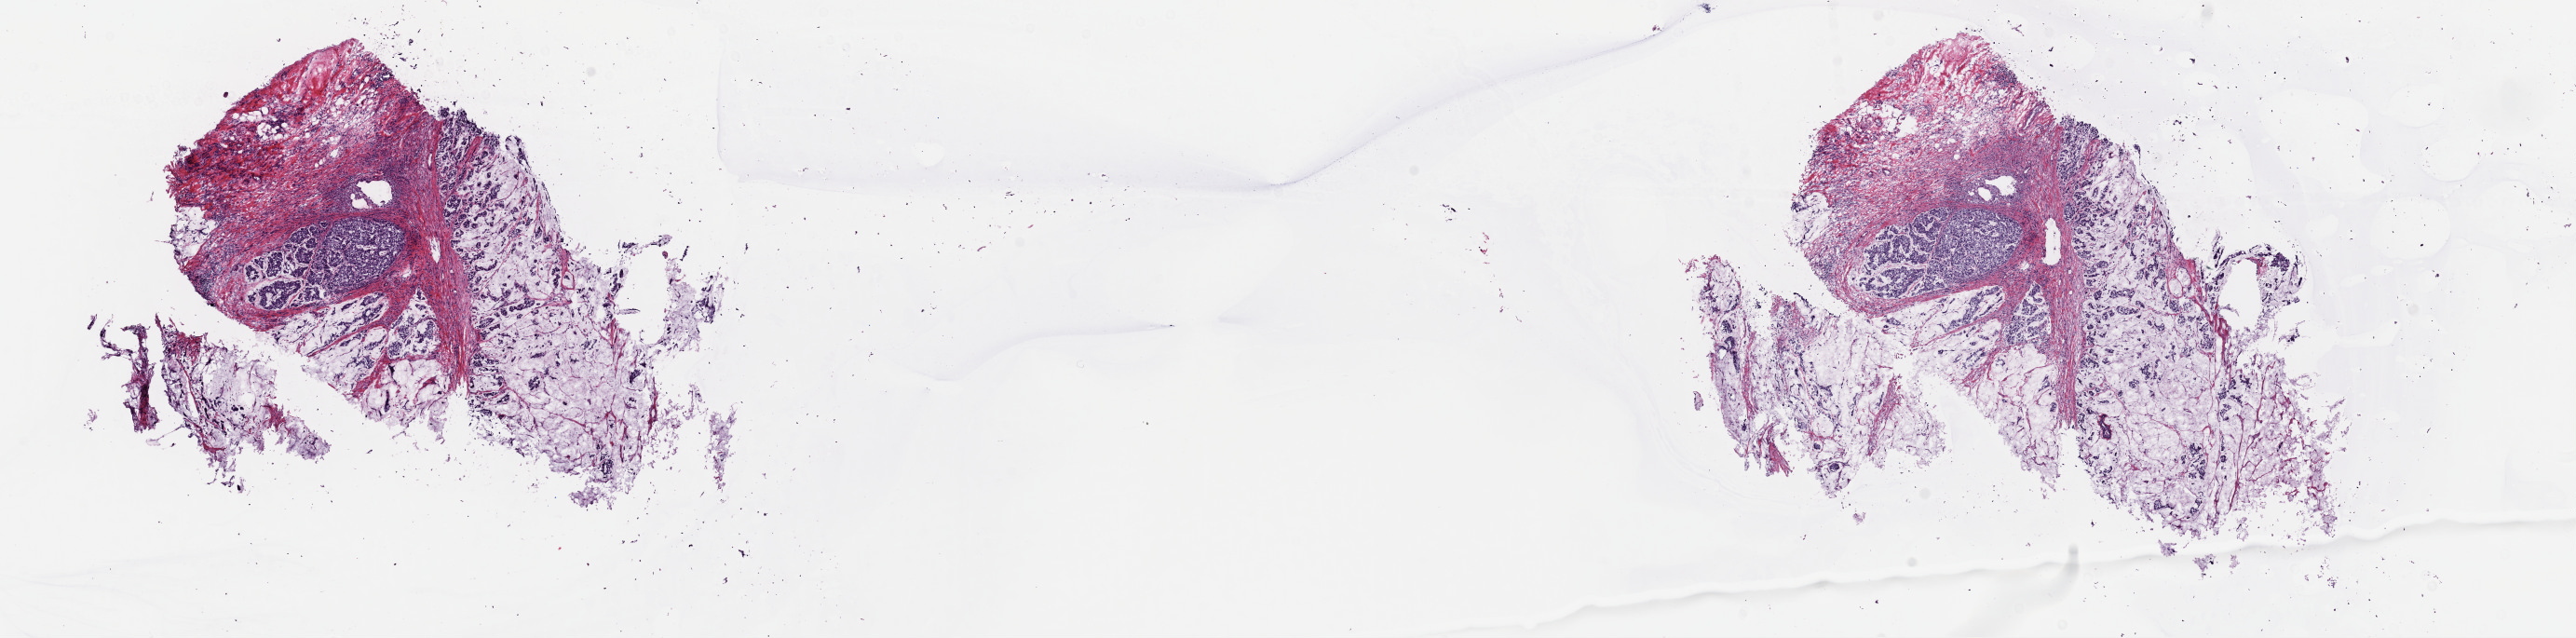
Hematoxylin and eosin (H&E) stained whole-slide image — whole scanned area (about 21.9 x 5.4 mm, acquisition: 40x scan) shown as a low-resolution overview, frozen section, breast, primary tumour sample. Female, age 55 years at initial diagnosis. Composition of this section per pathologist review: tumour cells 40%, tumour nuclei 70%, normal cells 0%, stromal cells 60%, necrosis 0%. Infiltration values recorded for this section: lymphocyte infiltration 0%, monocyte infiltration 0%, neutrophil infiltration 0%.
Pathologic diagnosis: Mucinous adenocarcinoma. Lymph nodes positive (case pathology): 0 of 12 examined. AJCC pathologic stage: IIIB.